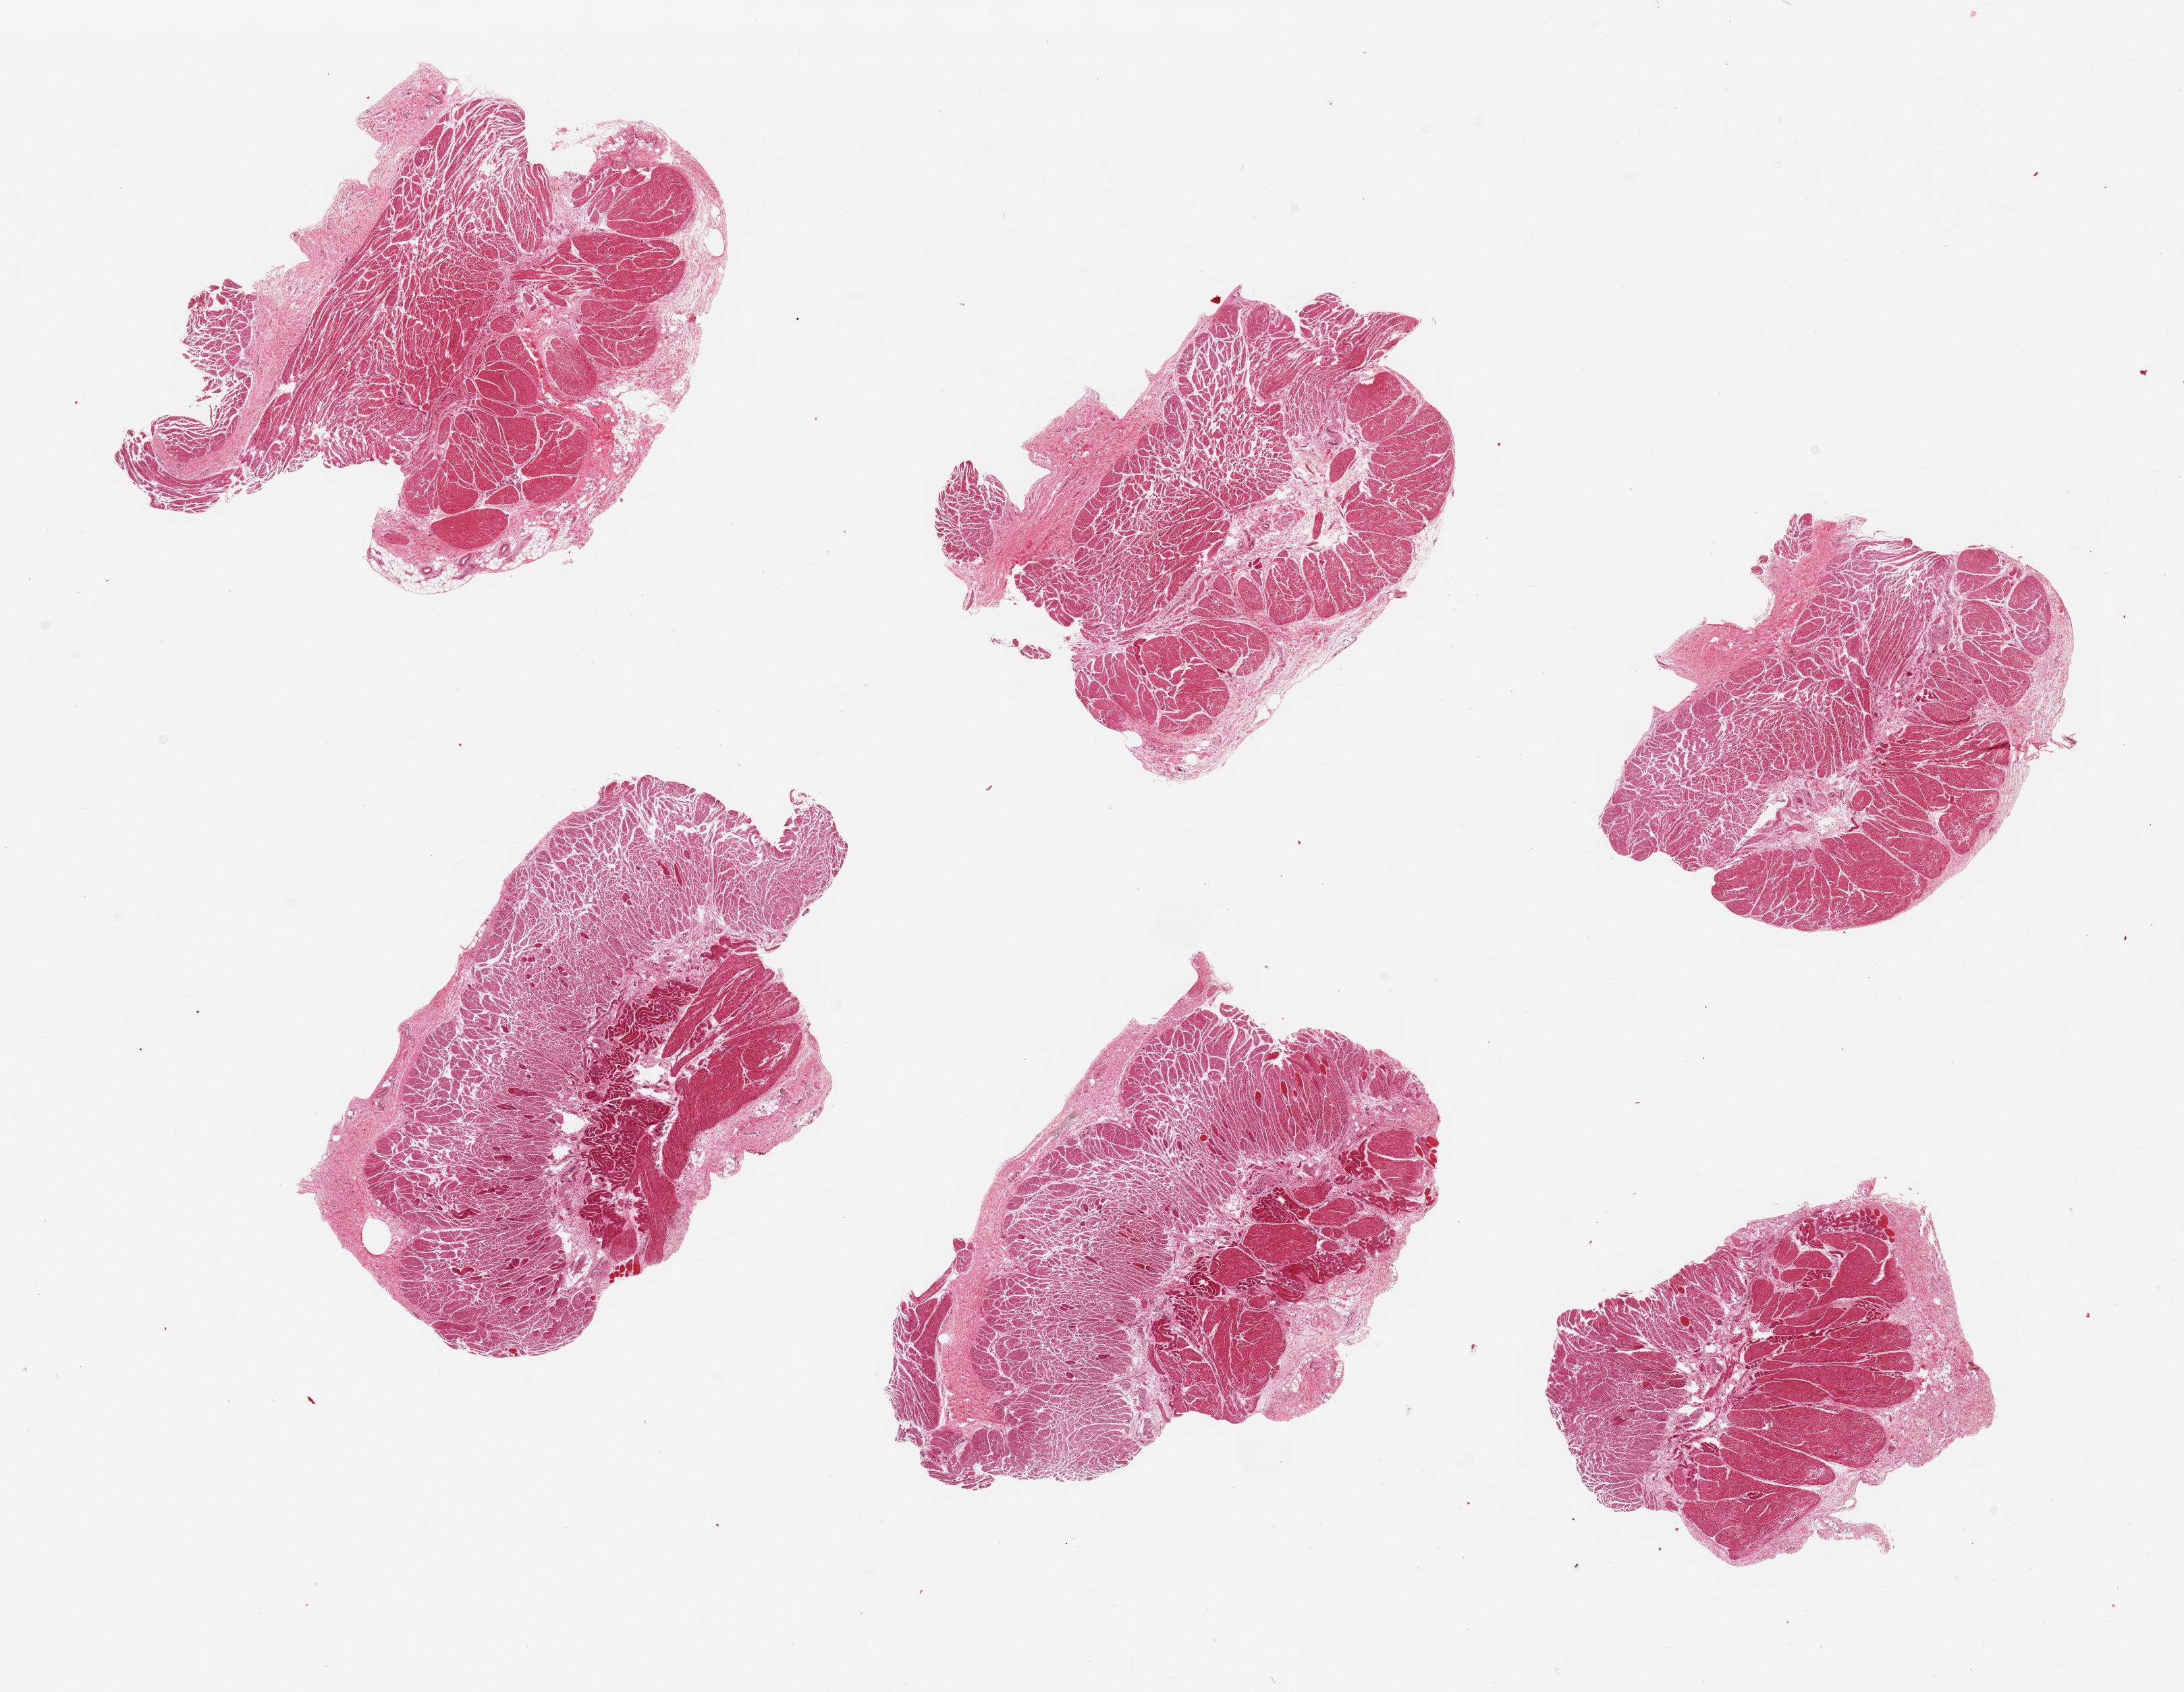
Hematoxylin and eosin (H&E) whole-slide image, brightfield — a low-resolution overview of the entire scanned area, about 25.6 x 19.8 mm; PAXgene-fixed paraffin-embedded (PFPE) section; target tissue: esophageal muscle; tissue donor sample. Male donor.
Review note (as recorded): 6 pieces, no residual mucosa.